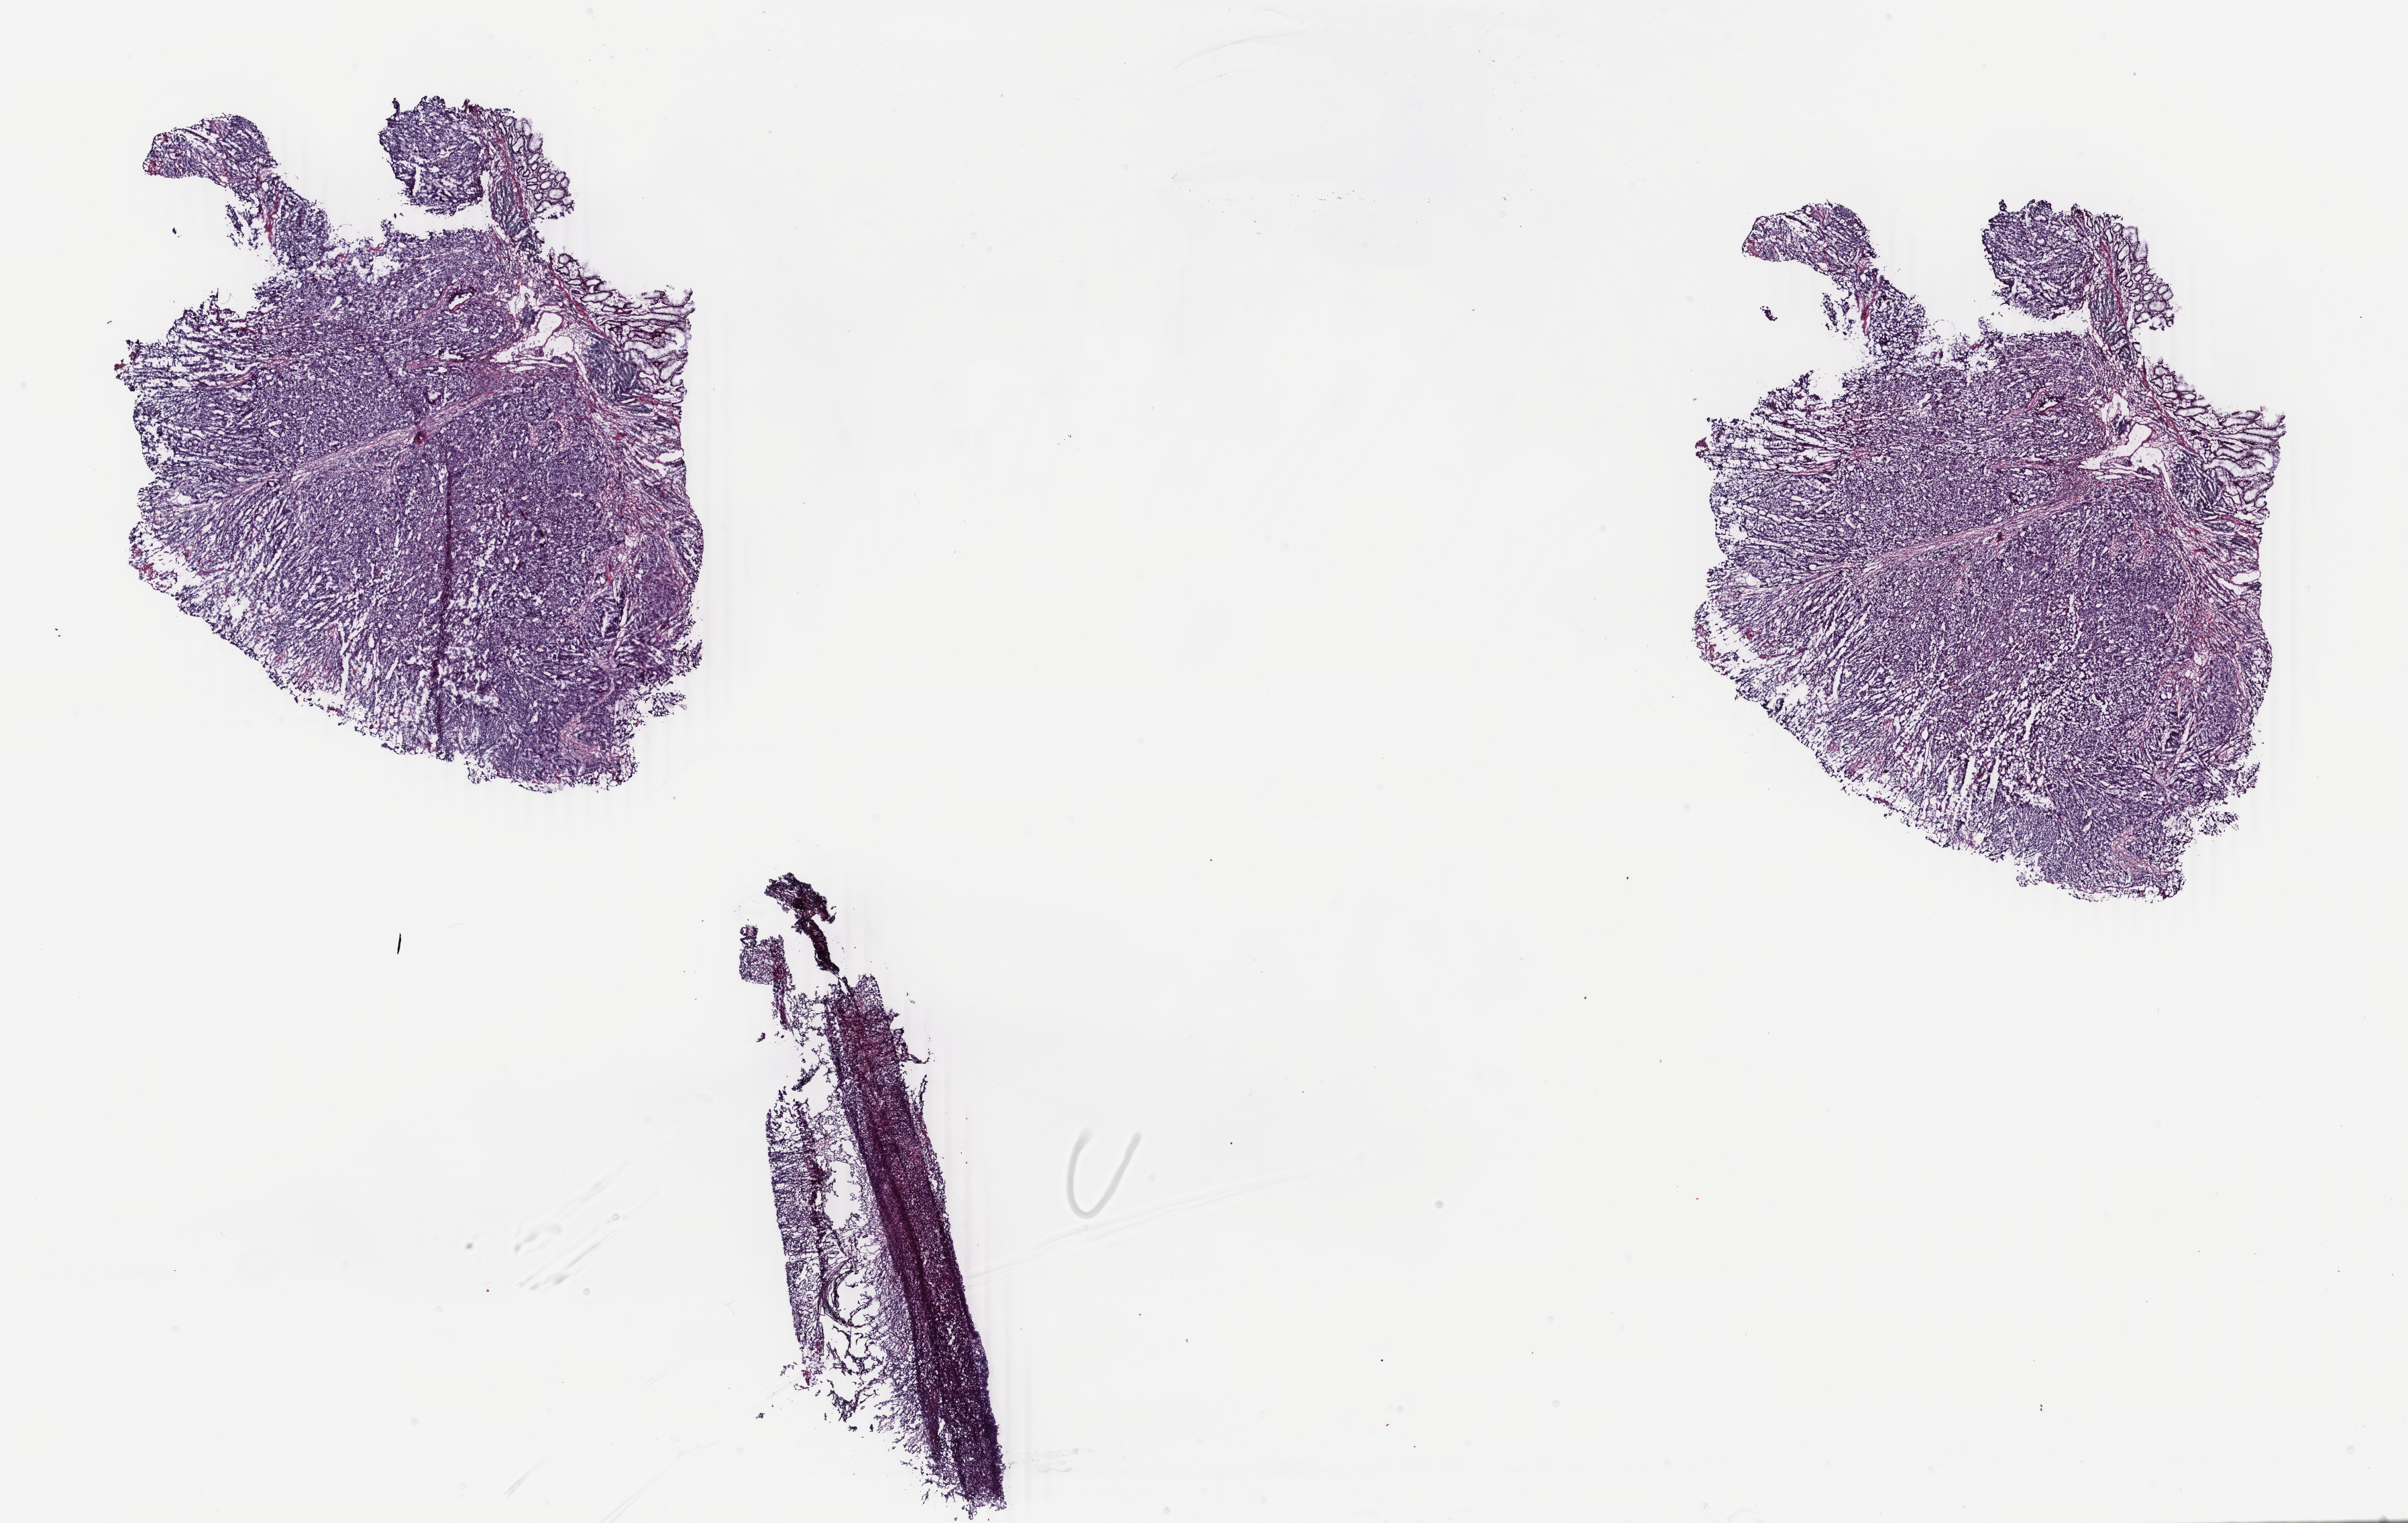
Digitized H&E tissue section (whole slide) — low-resolution overview of the scanned area, about 28.6 x 18.1 mm, frozen section from the top of the tissue portion, colon, primary tumour sample. Patient: female, age at initial diagnosis 46 years. Pathologist review of this section (percent, as recorded): tumour cells 80%, tumour nuclei 75%, normal cells 7%, stromal cells 11%, necrosis 2%. Infiltration values recorded for this section: lymphocyte infiltration 13%, monocyte infiltration 1%, neutrophil infiltration 2%.
Lymph nodes positive (case pathology): 0 of 45 examined. AJCC pathologic stage: IIB (6th edition). Diagnosis: Adenocarcinoma, NOS (transverse colon).